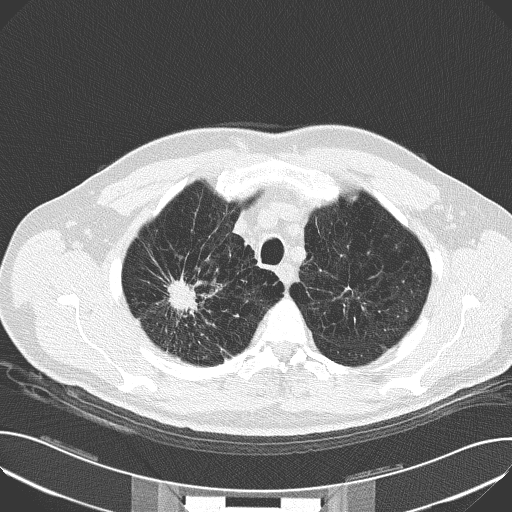
Chest CT (low-dose screening protocol), one axial image; baseline annual screen; lung window (W 1500 / L -600 HU); 512 × 512 image matrix, field of view 380 × 380 mm. Male, age 59 years at enrolment.
Expert reader's lesion annotation, bounding box [x1, y1, x2, y2] px = [154, 260, 217, 327]. The screening reader recorded 4 non-calcified nodules or masses ≥4 mm on this exam; which of them this box marks is not recorded. Official screen result: positive, change unspecified: nodule(s) >= 4 mm or enlarging nodule(s), mass(es), or other non-specific abnormalities suspicious for lung cancer. Lung cancer was diagnosed 44 days after this screen: squamous cell carcinoma, NOS, right upper lobe, moderately differentiated (G2), stage IA (AJCC 6th edition), 30 mm at pathology.